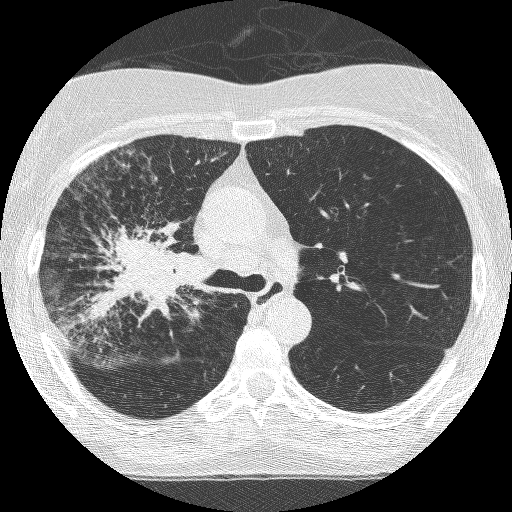
Low-dose screening chest CT, axial slice; third screening round (two years after baseline); lung window (W 1500 / L -600 HU); 1.25 mm slice thickness. Female, age 64 years at enrolment.
Expert-annotated lung lesion, bounding box <87,217,205,335> (left, top, right, bottom; pixels). The exam's reader record, not a measurement of the box and not confirmed to be the same lesion: non-calcified nodule or mass ≥4 mm, right upper lobe, 49 × 43 mm, spiculated (stellate) margins, soft tissue attenuation, pre-existing on the prior screen: yes; interval growth: yes. Official screen result: positive, other. Later outcome: lung cancer diagnosed 7 days after this screen — adenocarcinoma, NOS, right upper lobe, right middle lobe, right hilum, stage IV (AJCC 6th edition), 85 mm at pathology.